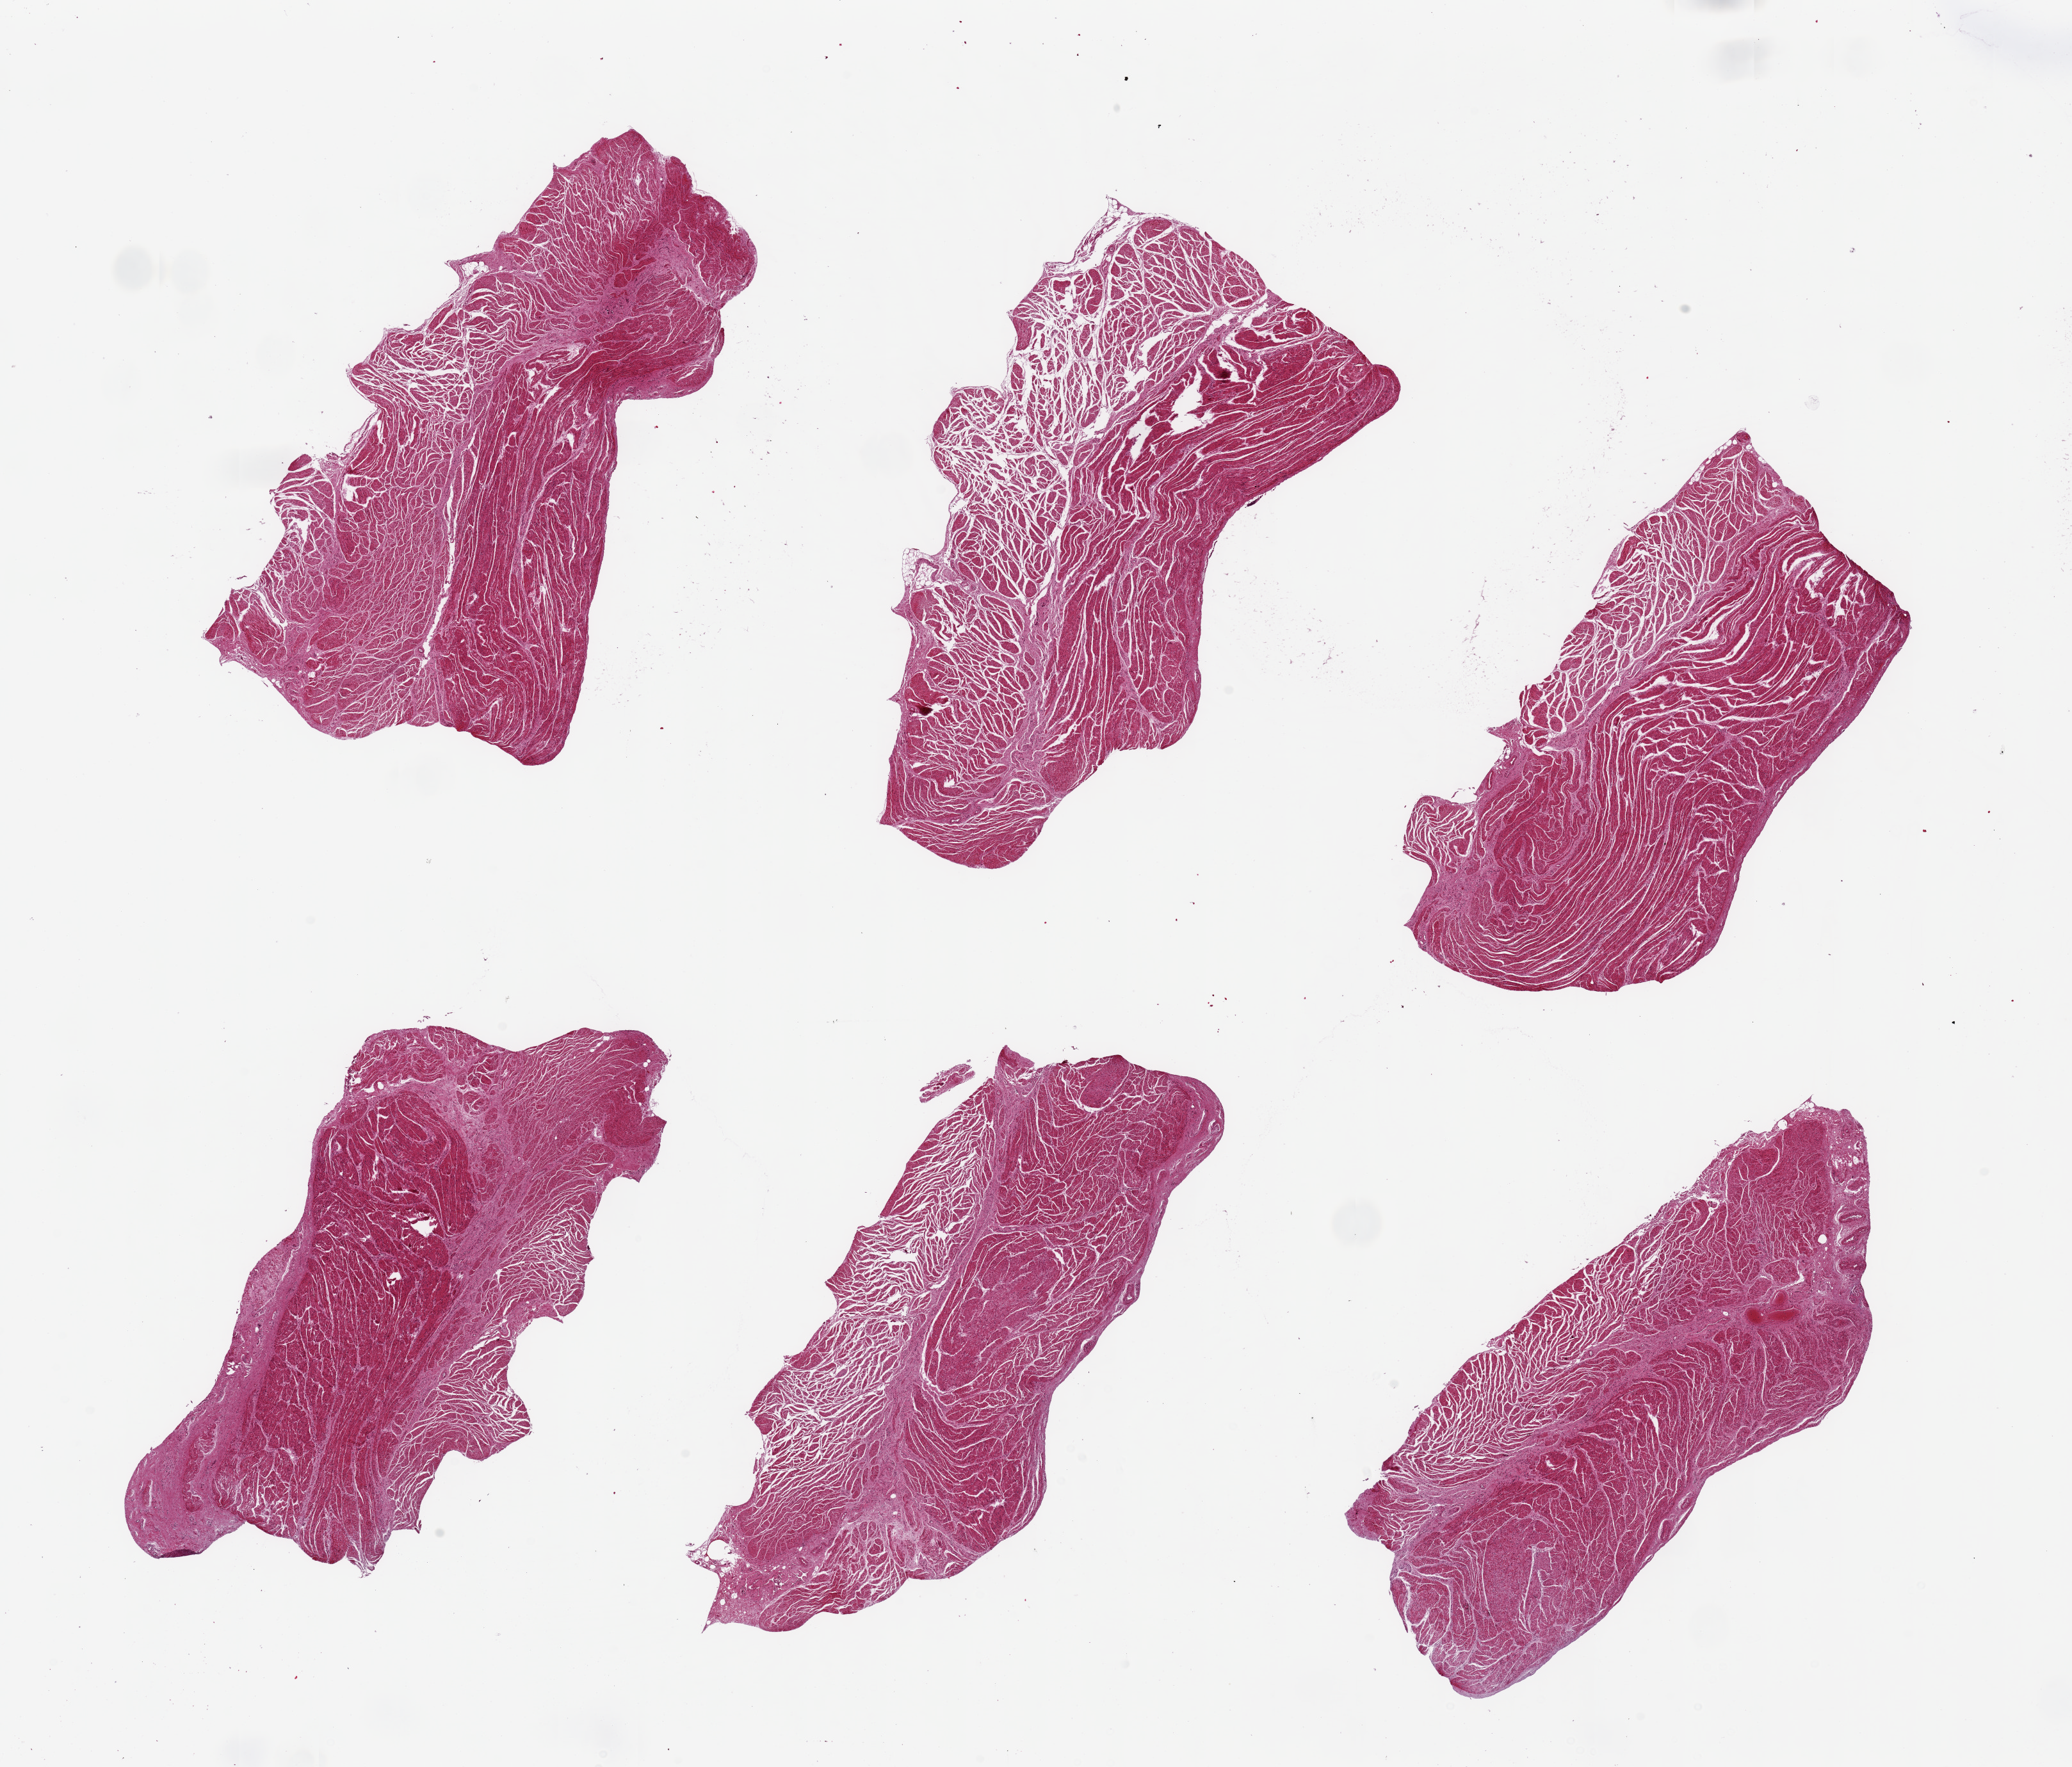
Whole-slide image, H&E stain, brightfield, whole scanned area (about 25.6 x 21.8 mm, acquisition: 20x scan) shown as a low-resolution overview; PAXgene-fixed paraffin-embedded (PFPE) section; sampled site (target tissue): gastroesophageal junction; tissue donor sample. Donor sex: female.
• reviewer comment on this tissue sample: 6 pieces, up to 8x3mm; muscle show loss of cohesion